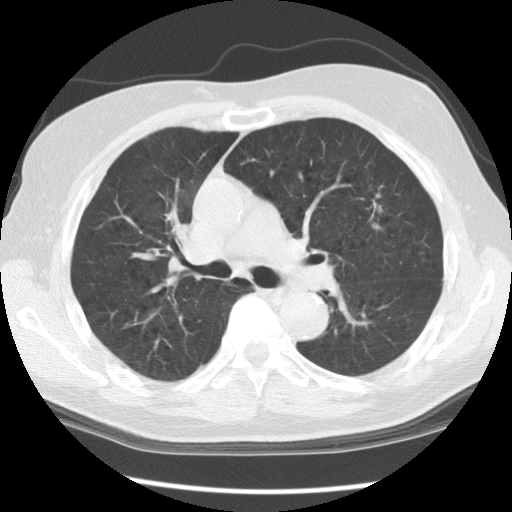
Chest CT (low-dose screening protocol), one axial image, second annual screen, lung window (W 1500 / L -600 HU), 2.5 mm slice thickness. Male, age 70 years at enrolment.
Expert reader's lesion annotation, bounding box (x1, y1, x2, y2) in pixels: (341, 180, 401, 235). The screening reader recorded 3 non-calcified nodules or masses ≥4 mm on this exam (right lower lobe, left upper lobe, left upper lobe); which of them this box marks is not recorded. Official screen result: positive, other. Later outcome: lung cancer diagnosed 396 days after this screen (after the third annual screen) — adenocarcinoma, NOS, left upper lobe, moderately differentiated (G2), stage IIIA (AJCC 6th edition), 17 mm at pathology.